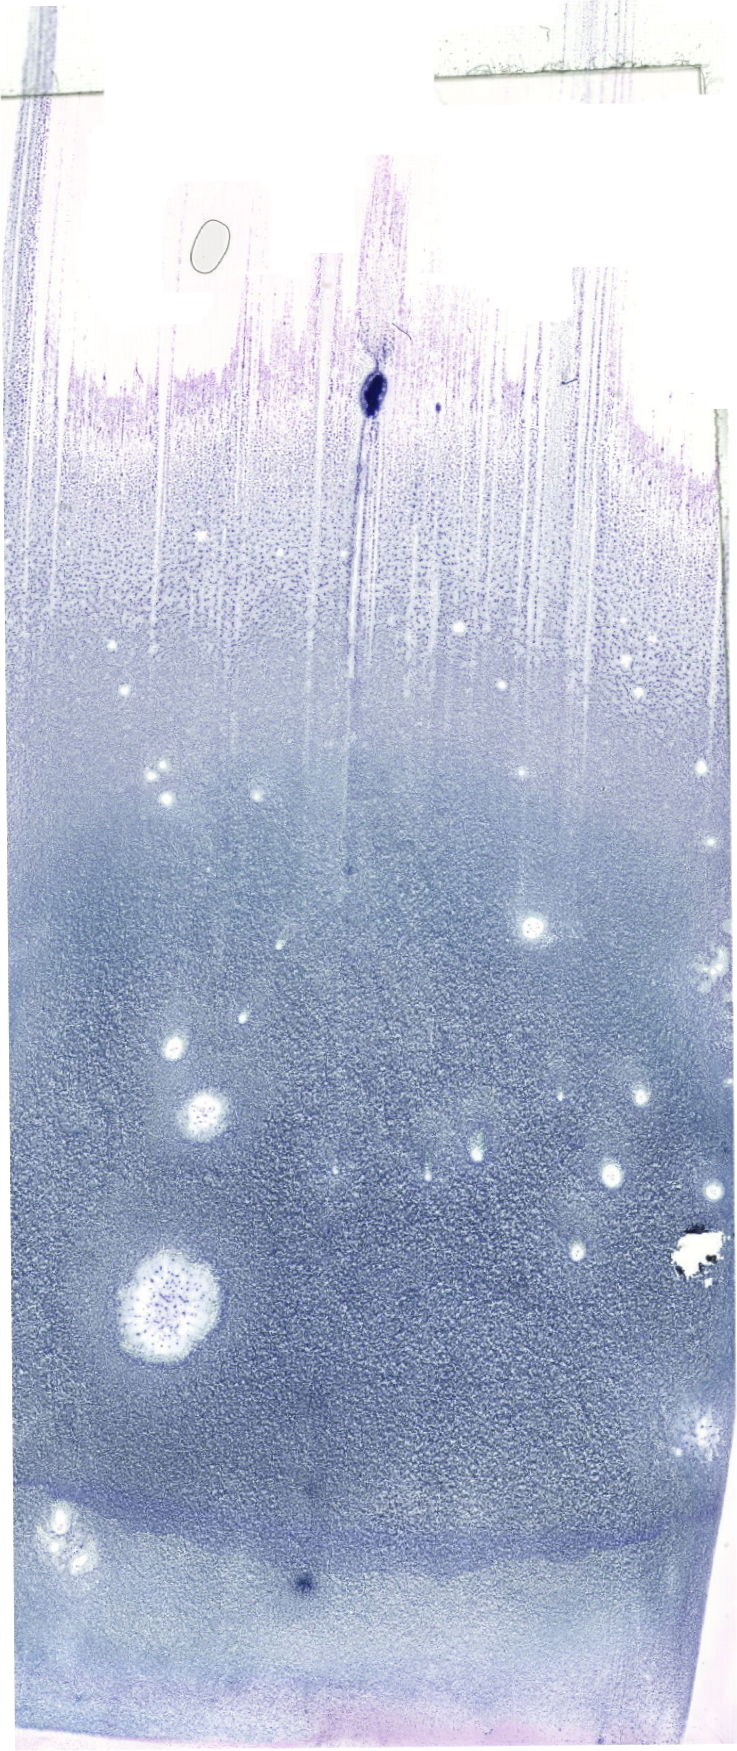
May-Grünwald-Giemsa (MGG)-stained marrow aspirate smear (whole slide) — a low-resolution overview of the entire scanned area, about 20.9 x 49.6 mm. Patient sex: male.
Diagnosis: B Acute Lymphoblastic Leukemia.